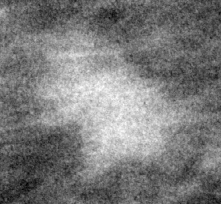
Cropped region of a digitized screen-film mammogram centred on a radiologist-marked abnormality; right breast; MLO view.
Mass, shape irregular, margins ill defined; BI-RADS assessment category 4; pathology result (as recorded, not read from the image): malignant.